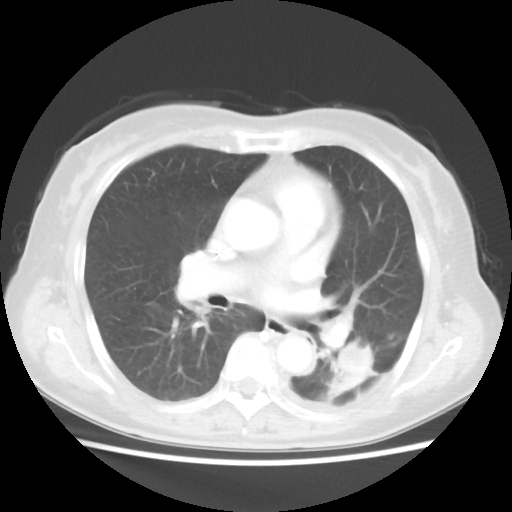
Chest CT, one axial slice. Position 20 of 40 along the scan axis. Reconstruction kernel STANDARD. 100 kVp. Lung window (W 1500 / L -600 HU). 5 mm slice thickness. 512 × 512 image matrix, field of view 341 × 341 mm. Patient: female, 69 years. Case-level facts recorded for this patient, not image findings: clinical TNM (as recorded): T1c N0 M0.
Outlined on this slice (rectangle marked by the reading radiologist):
- lung tumour (recorded histology: adenocarcinoma): bounding box [x1, y1, x2, y2] px = [328, 341, 380, 404]